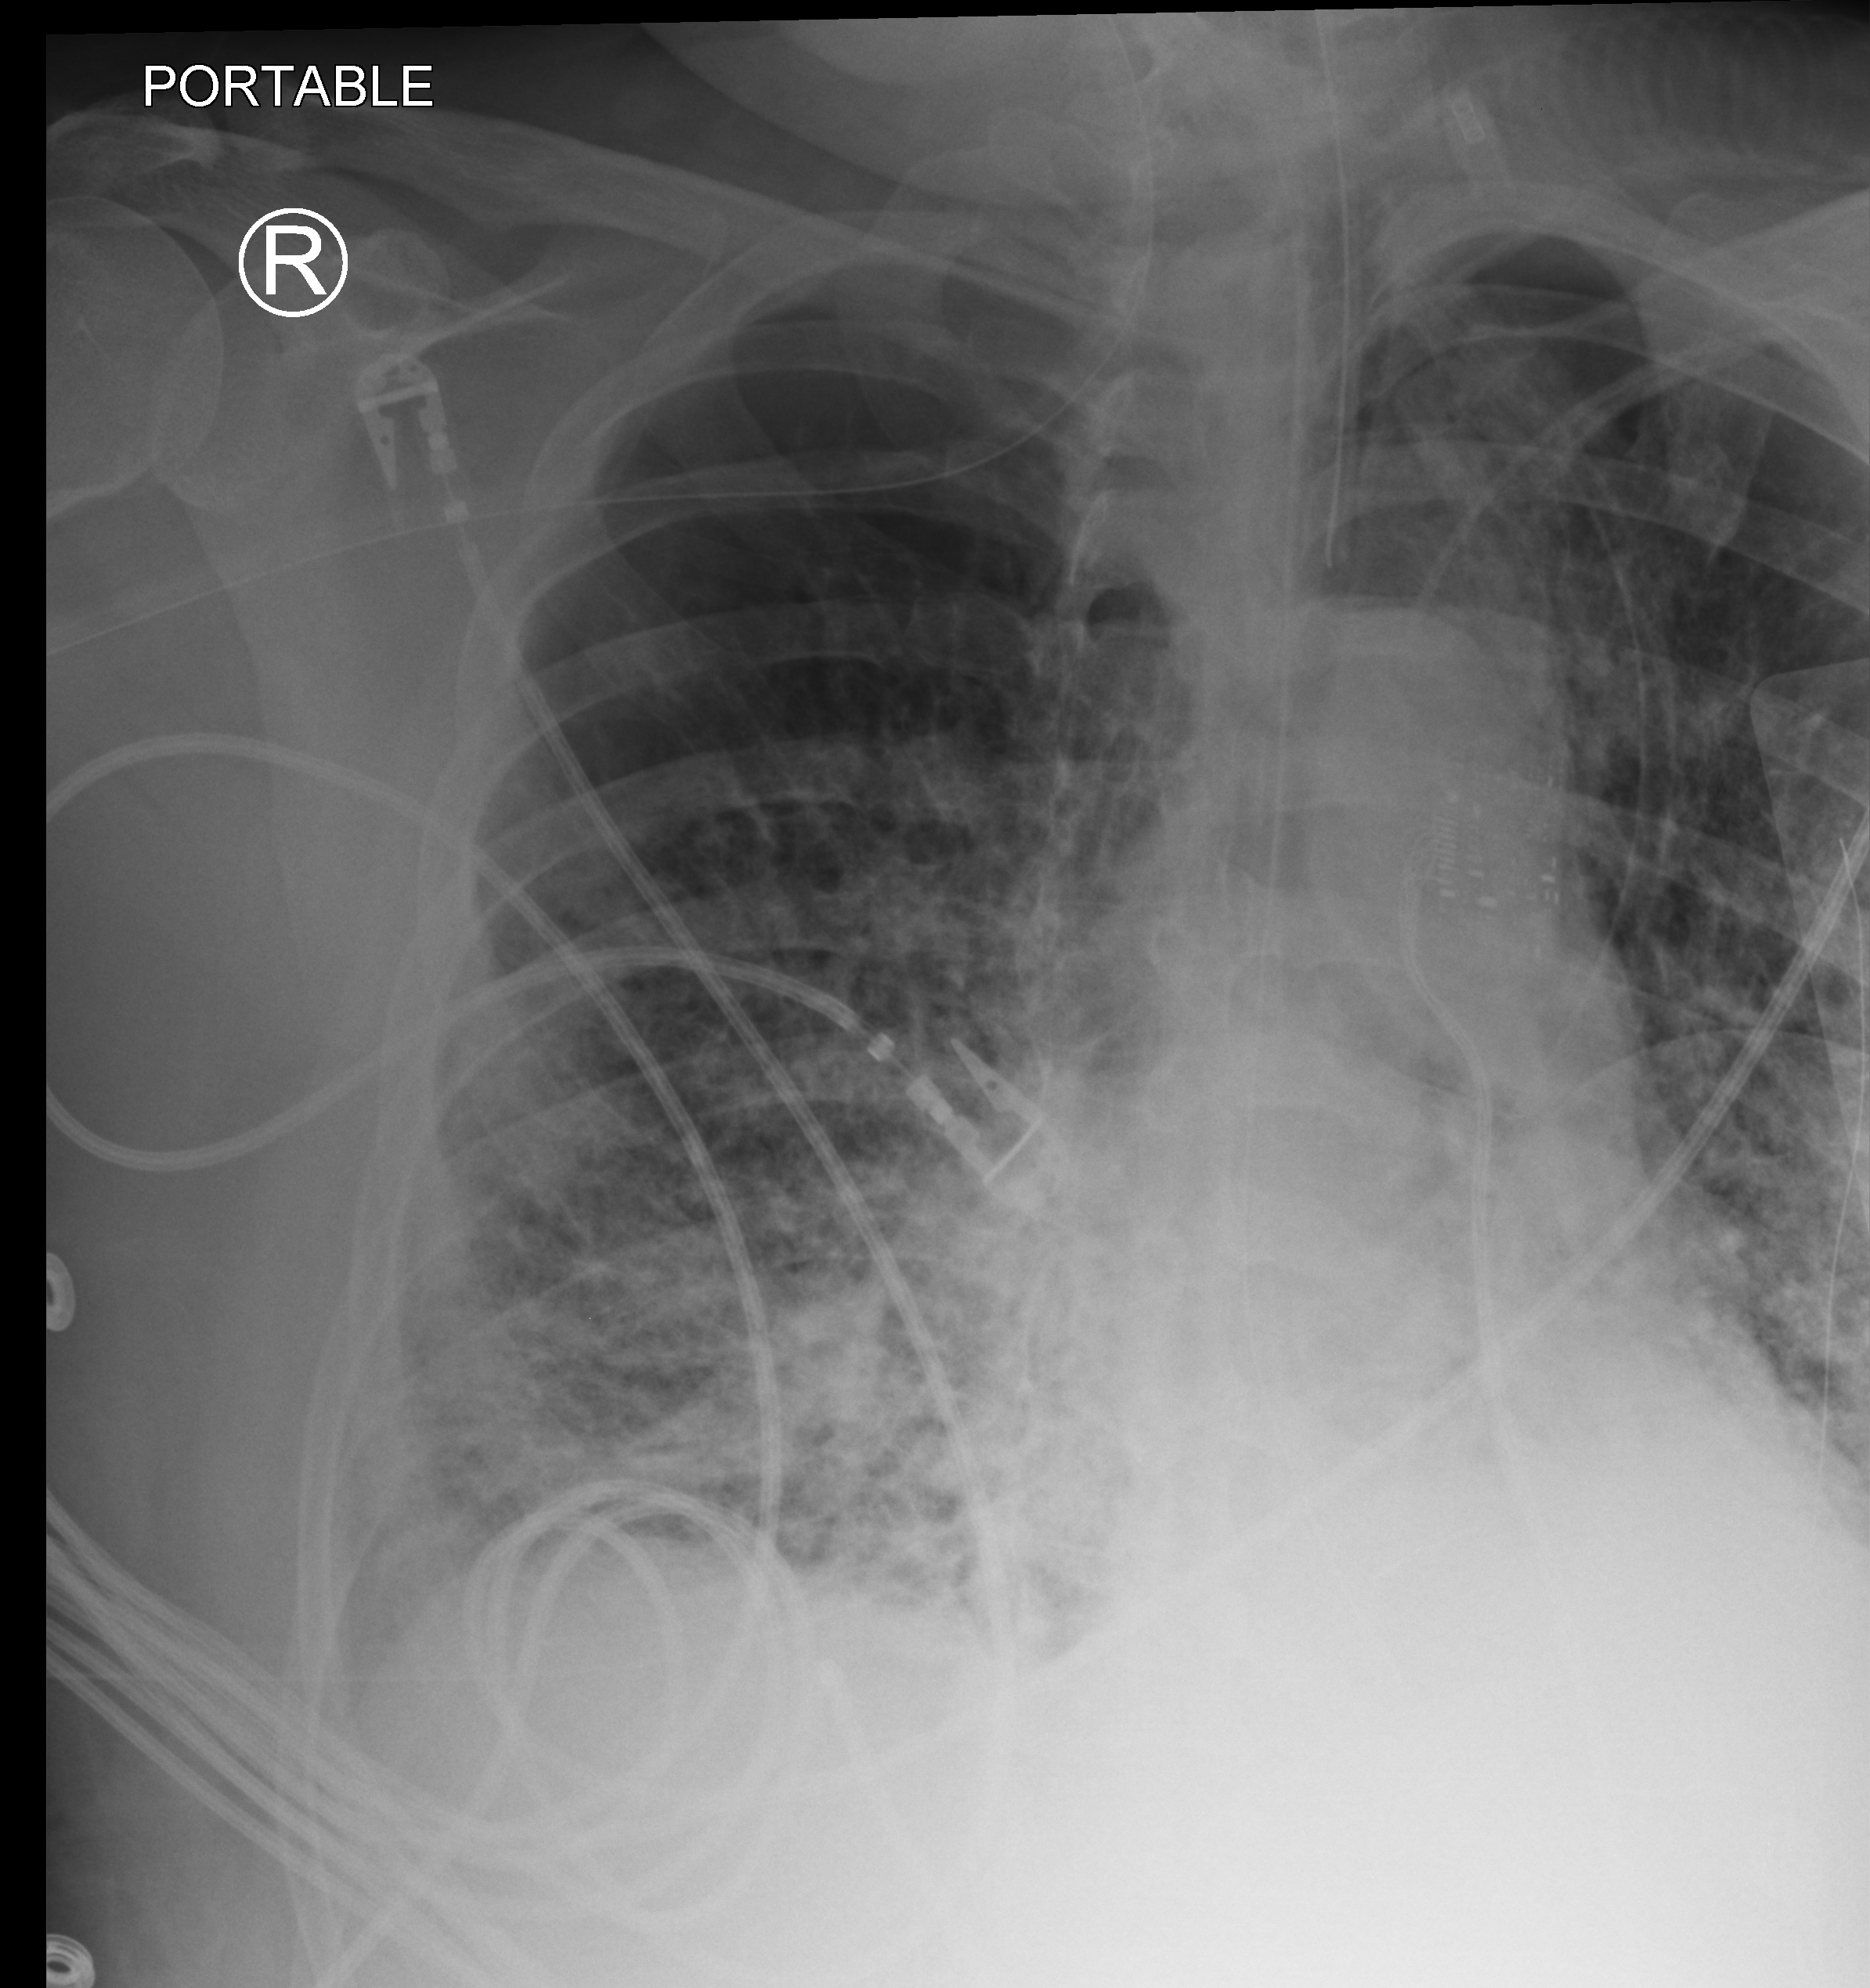
Bedside chest radiograph (computed radiography). Patient hospitalised with COVID-19, aged 18–59 years.
Hospital-stay facts (about this admission, not read from this image; timing relative to this image not recorded): admitted to intensive care during this hospital stay: yes.